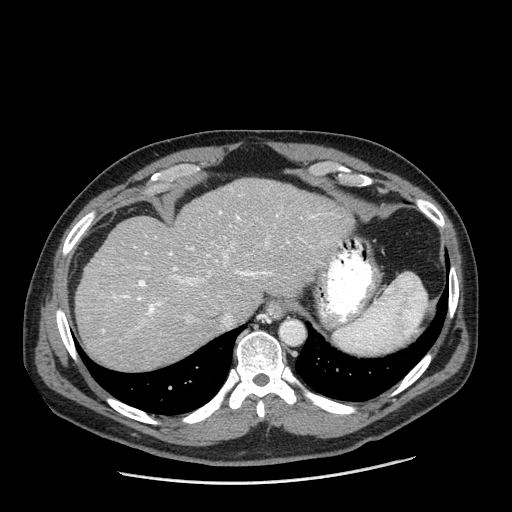
Contrast-enhanced abdominal CT (liver protocol), one axial slice. 120 kVp. One of 2 acquisitions stored at this slice position. Soft-tissue window (W 400 / L 40 HU). 2.5 mm slice thickness. 512 × 512 image matrix. Case-level facts recorded for this patient, not image findings: diagnosis: hepatocellular carcinoma (patient treated with transarterial chemoembolisation; whether this scan precedes or follows treatment is not stated here); TNM stage (as recorded): Stage-II; Child-Pugh class: A; tumour differentiation: moderately differentiated; tumour nodularity: multinodular.
Structures marked on this image (semi-automatic segmentation, software-assisted and operator-edited):
- abdominal aorta: box from (x=280, y=321) to (x=304, y=344) px
- liver parenchyma outside the tumour (the mass and vessels are separate outlines, so this box may not span the whole liver): (x=74, y=178)–(x=354, y=370)
- liver vessels: (x=102, y=211)–(x=332, y=333)